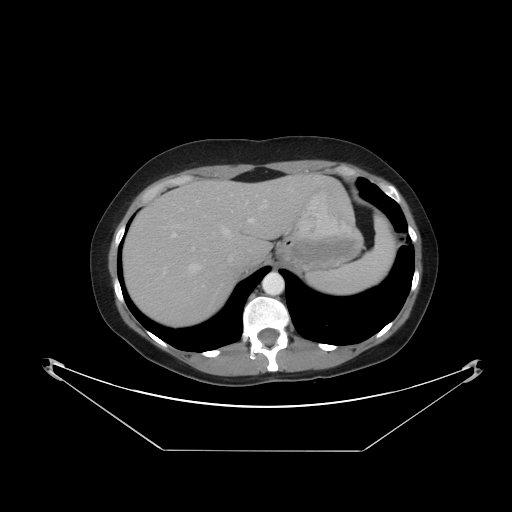
Contrast-enhanced abdominal CT, one axial slice. 120 kVp. Intravenous contrast given. Soft-tissue window (W 400 / L 40 HU). 5 mm slice thickness. 512 × 512 image matrix, field of view 482 × 482 mm. Female patient, age 38 years. From the clinical record (not read from this slice): diagnosis: colorectal cancer liver metastases, imaged before liver resection; multiple liver metastases: yes; largest metastasis: 2.5 cm; disease in both lobes: no.
Outlined on this slice (manually delineated by an expert):
- hepatic veins: box from (x=190, y=200) to (x=269, y=272) px
- liver: (x=123, y=177)–(x=354, y=328)
- planned liver remnant (the part of the liver to remain after resection): (x=191, y=177)–(x=354, y=260)
- portal vein (with intrahepatic branches): (x=172, y=200)–(x=266, y=261)